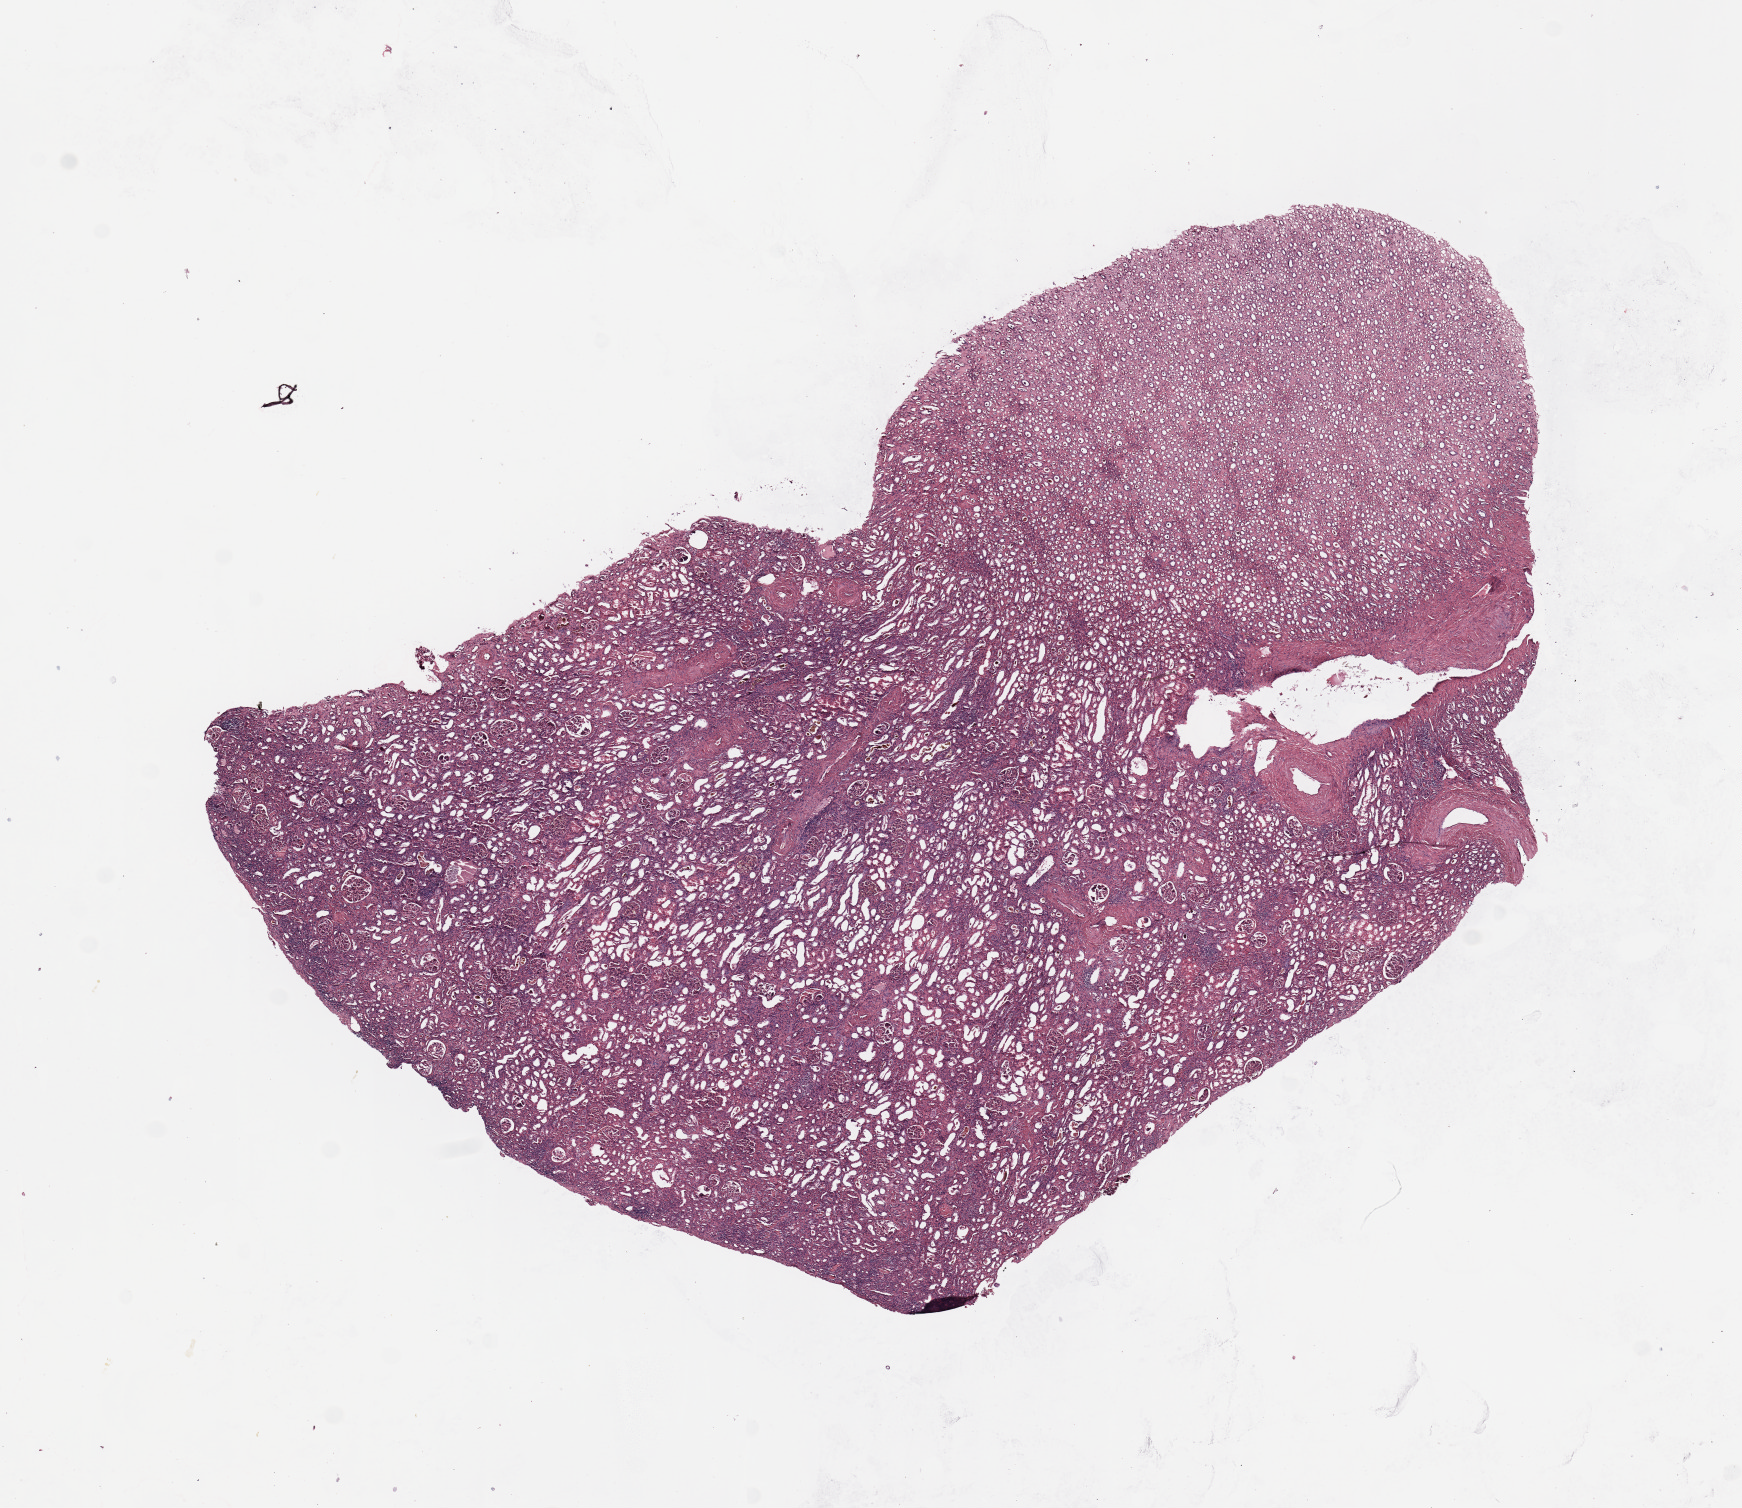
Whole-slide histology image, Hematoxylin and eosin (H&E) stained, a low-resolution overview of the entire scanned area, about 13.8 x 11.9 mm (from a 20x scan); normal (non-tumour) tissue sample, sampled site: kidney. Male, 61 y/o.
This section: normal (non-tumour) tissue from the same patient. Patient diagnosis: Renal cell carcinoma, NOS.